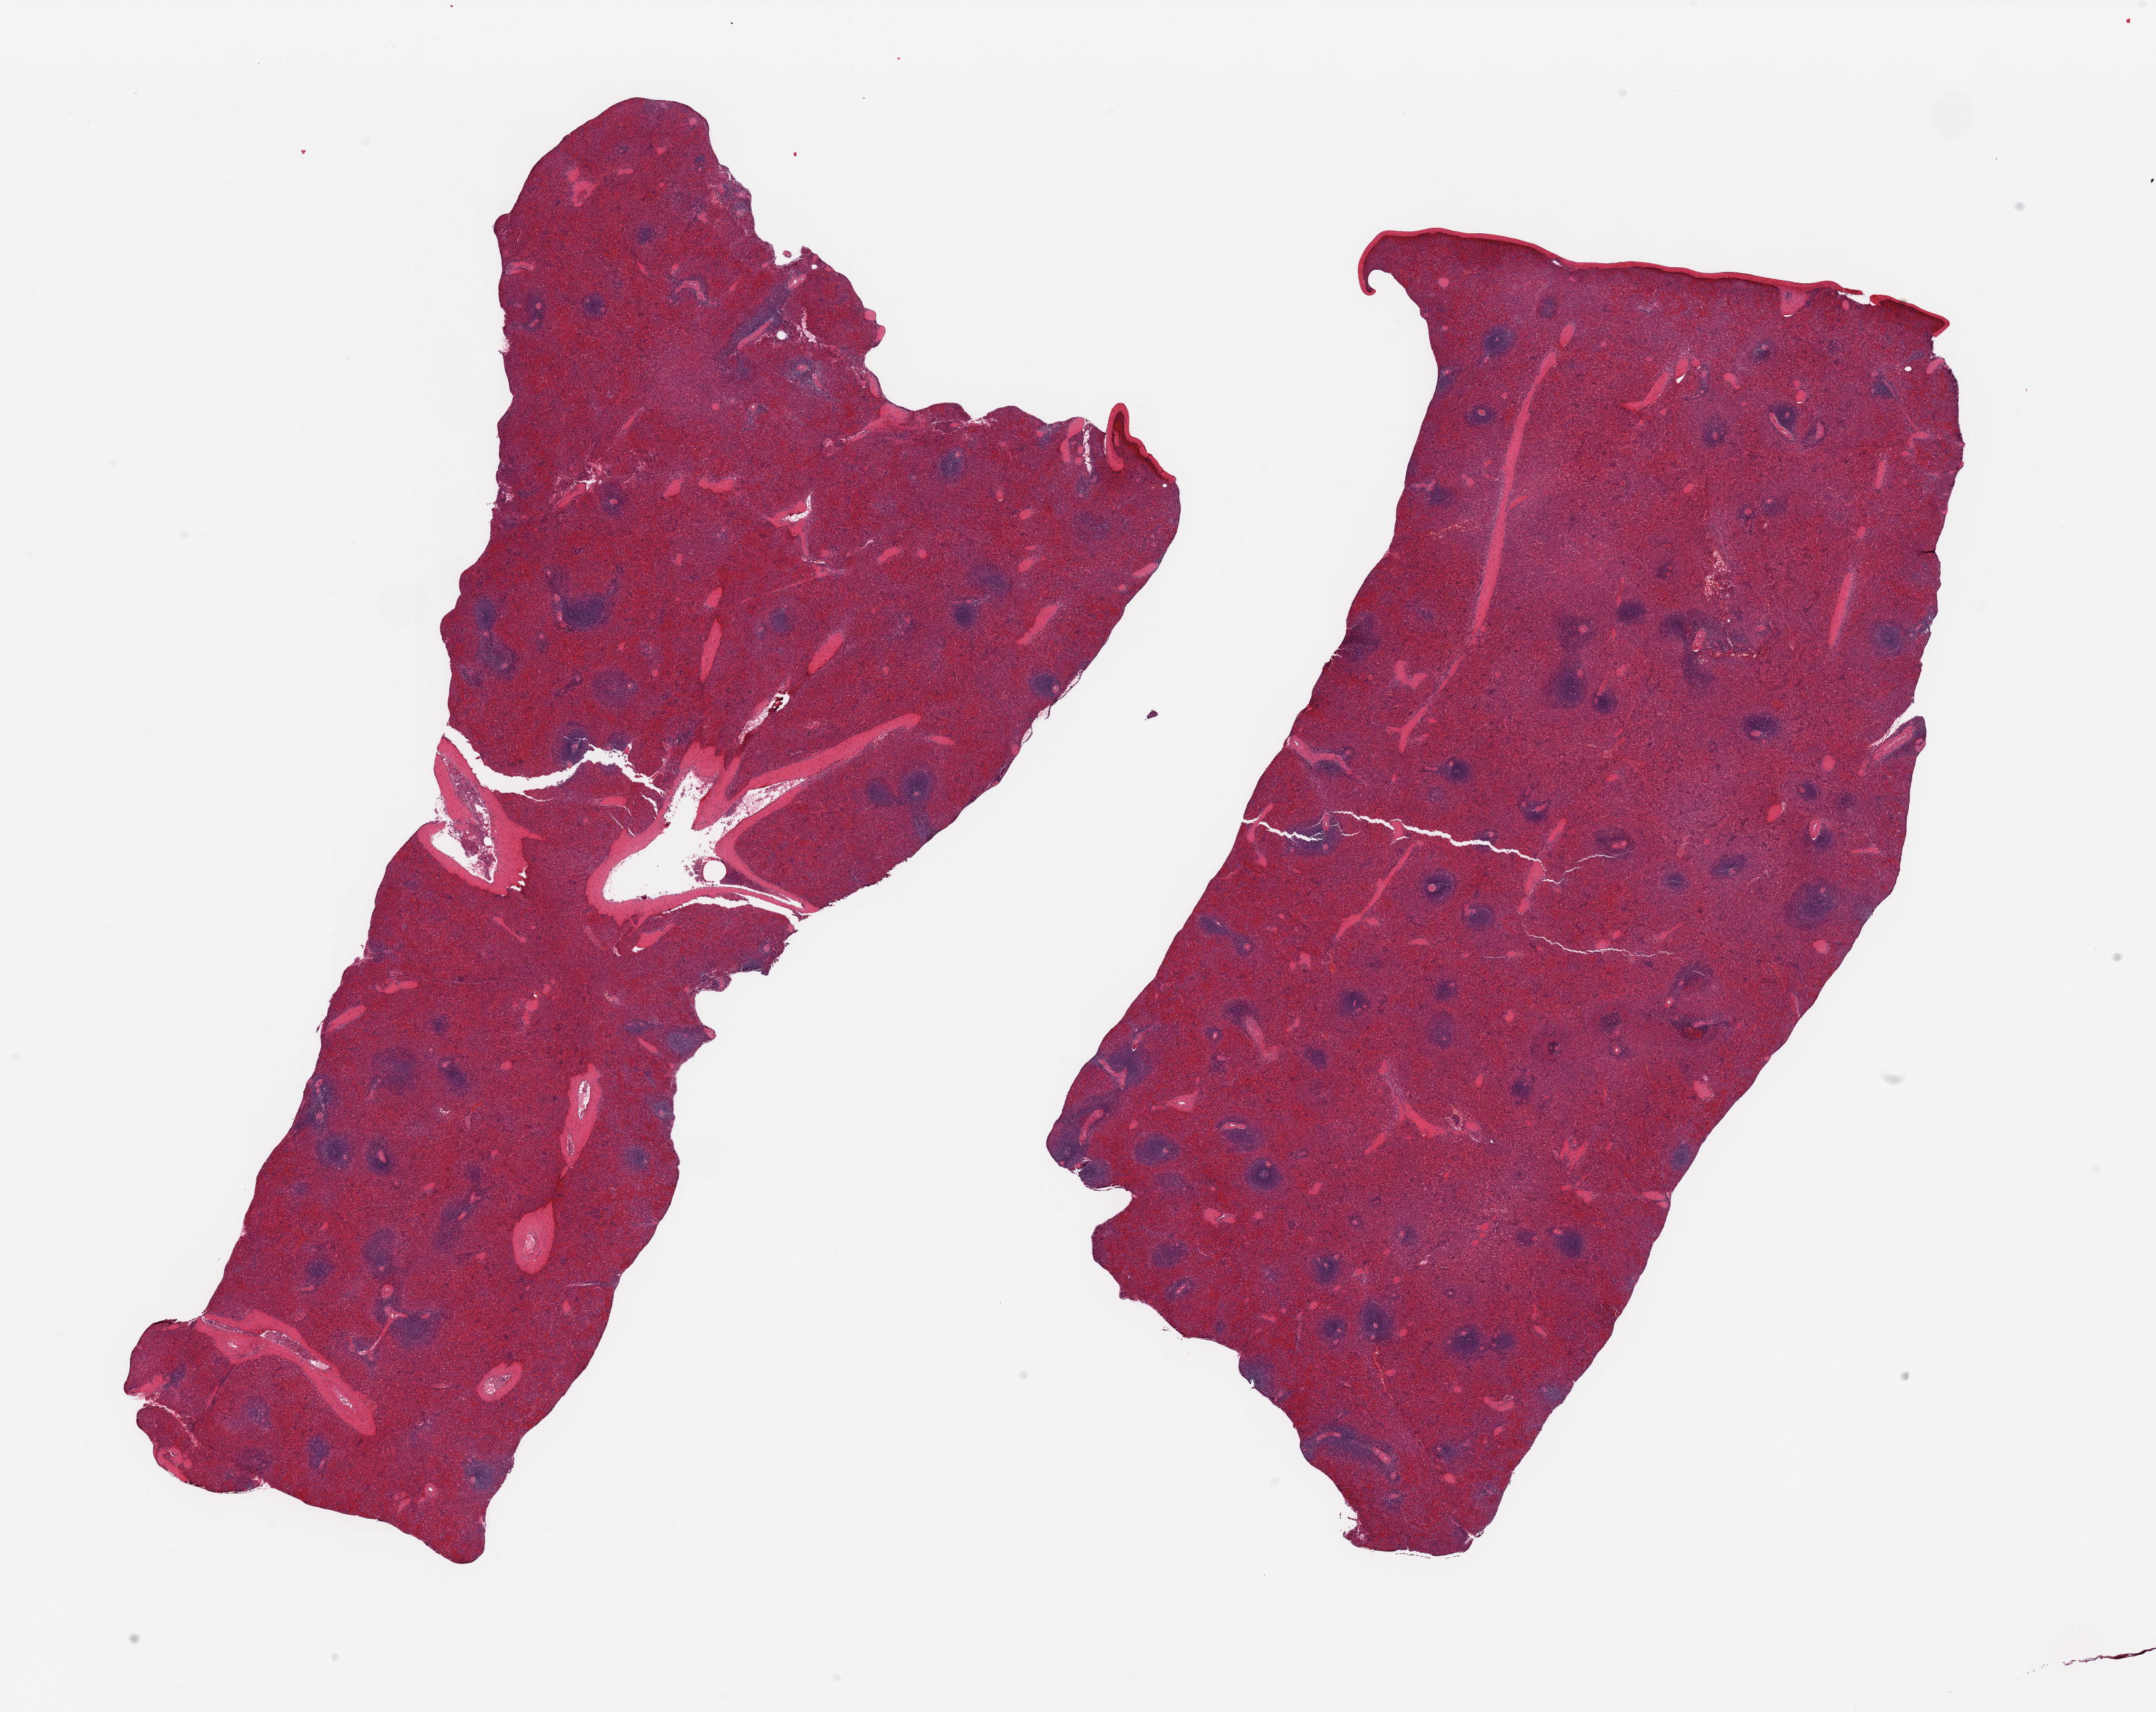
Whole-slide image, haematoxylin and eosin stain, a low-resolution overview of the entire scanned area, about 25.6 x 20.3 mm, PAXgene-fixed paraffin-embedded (PFPE) section, sampled site (target tissue): spleen, donor tissue sample.
Reviewer comment on this tissue sample: 2 pieces; congested, one piece includes capsule (target is 5mm below capsule).